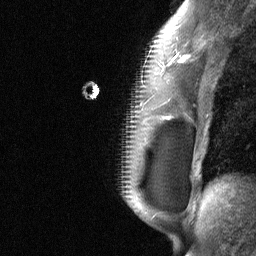
Breast MRI (dynamic contrast-enhanced), one sagittal slice. Position 45 of 64 along the scan axis. Dynamic contrast-enhanced study with each time point stored as its own series, time point 2 of 3 at this slice position (early post-contrast, ordered by acquisition time). 1.5 T. TE 4.8 ms, TR 27 ms. 2 mm slice thickness. 256 × 256 image matrix, field of view 200 × 200 mm. Patient: female, 34 years. Case-level facts recorded for this patient, not image findings: setting: breast cancer imaged before/during neoadjuvant chemotherapy; receptor status: HR-positive, HER2-negative.
Structures marked on this image (semi-automatic segmentation, software-assisted and operator-edited):
- analysis volume of interest (the breast-tissue region the enhancement analysis was run in; not a lesion): bounding box (x1, y1, x2, y2) in pixels: (92, 50, 188, 185)
- tumour enhancement mask (voxels above the 90 % enhancement threshold inside the analysis volume of interest): (168, 54, 184, 119)